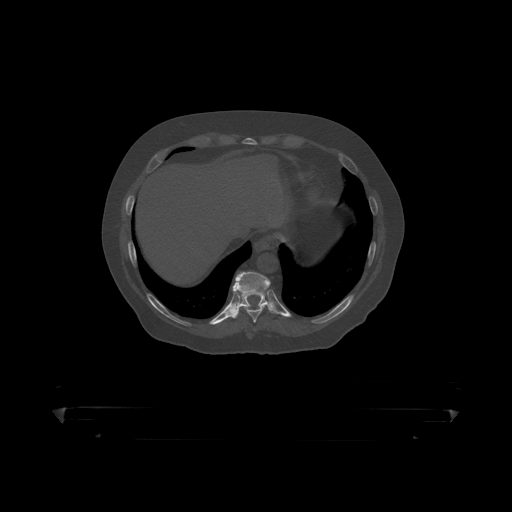
CT including the spine, one axial slice. Position 227 of 390 along the scan axis. Reconstruction kernel STANDARD. Bone window (W 1800 / L 400 HU). 512 × 512 image matrix, field of view 650 × 650 mm. Male patient, age 60 years. Case-level facts recorded for this patient, not image findings: primary cancer: prostate.
Structures marked on this image (semi-automatic segmentation, software-assisted and operator-edited):
- T10 vertebra: box from (x=235, y=272) to (x=271, y=308) px
- T9 vertebra: (x=232, y=285)–(x=268, y=319)